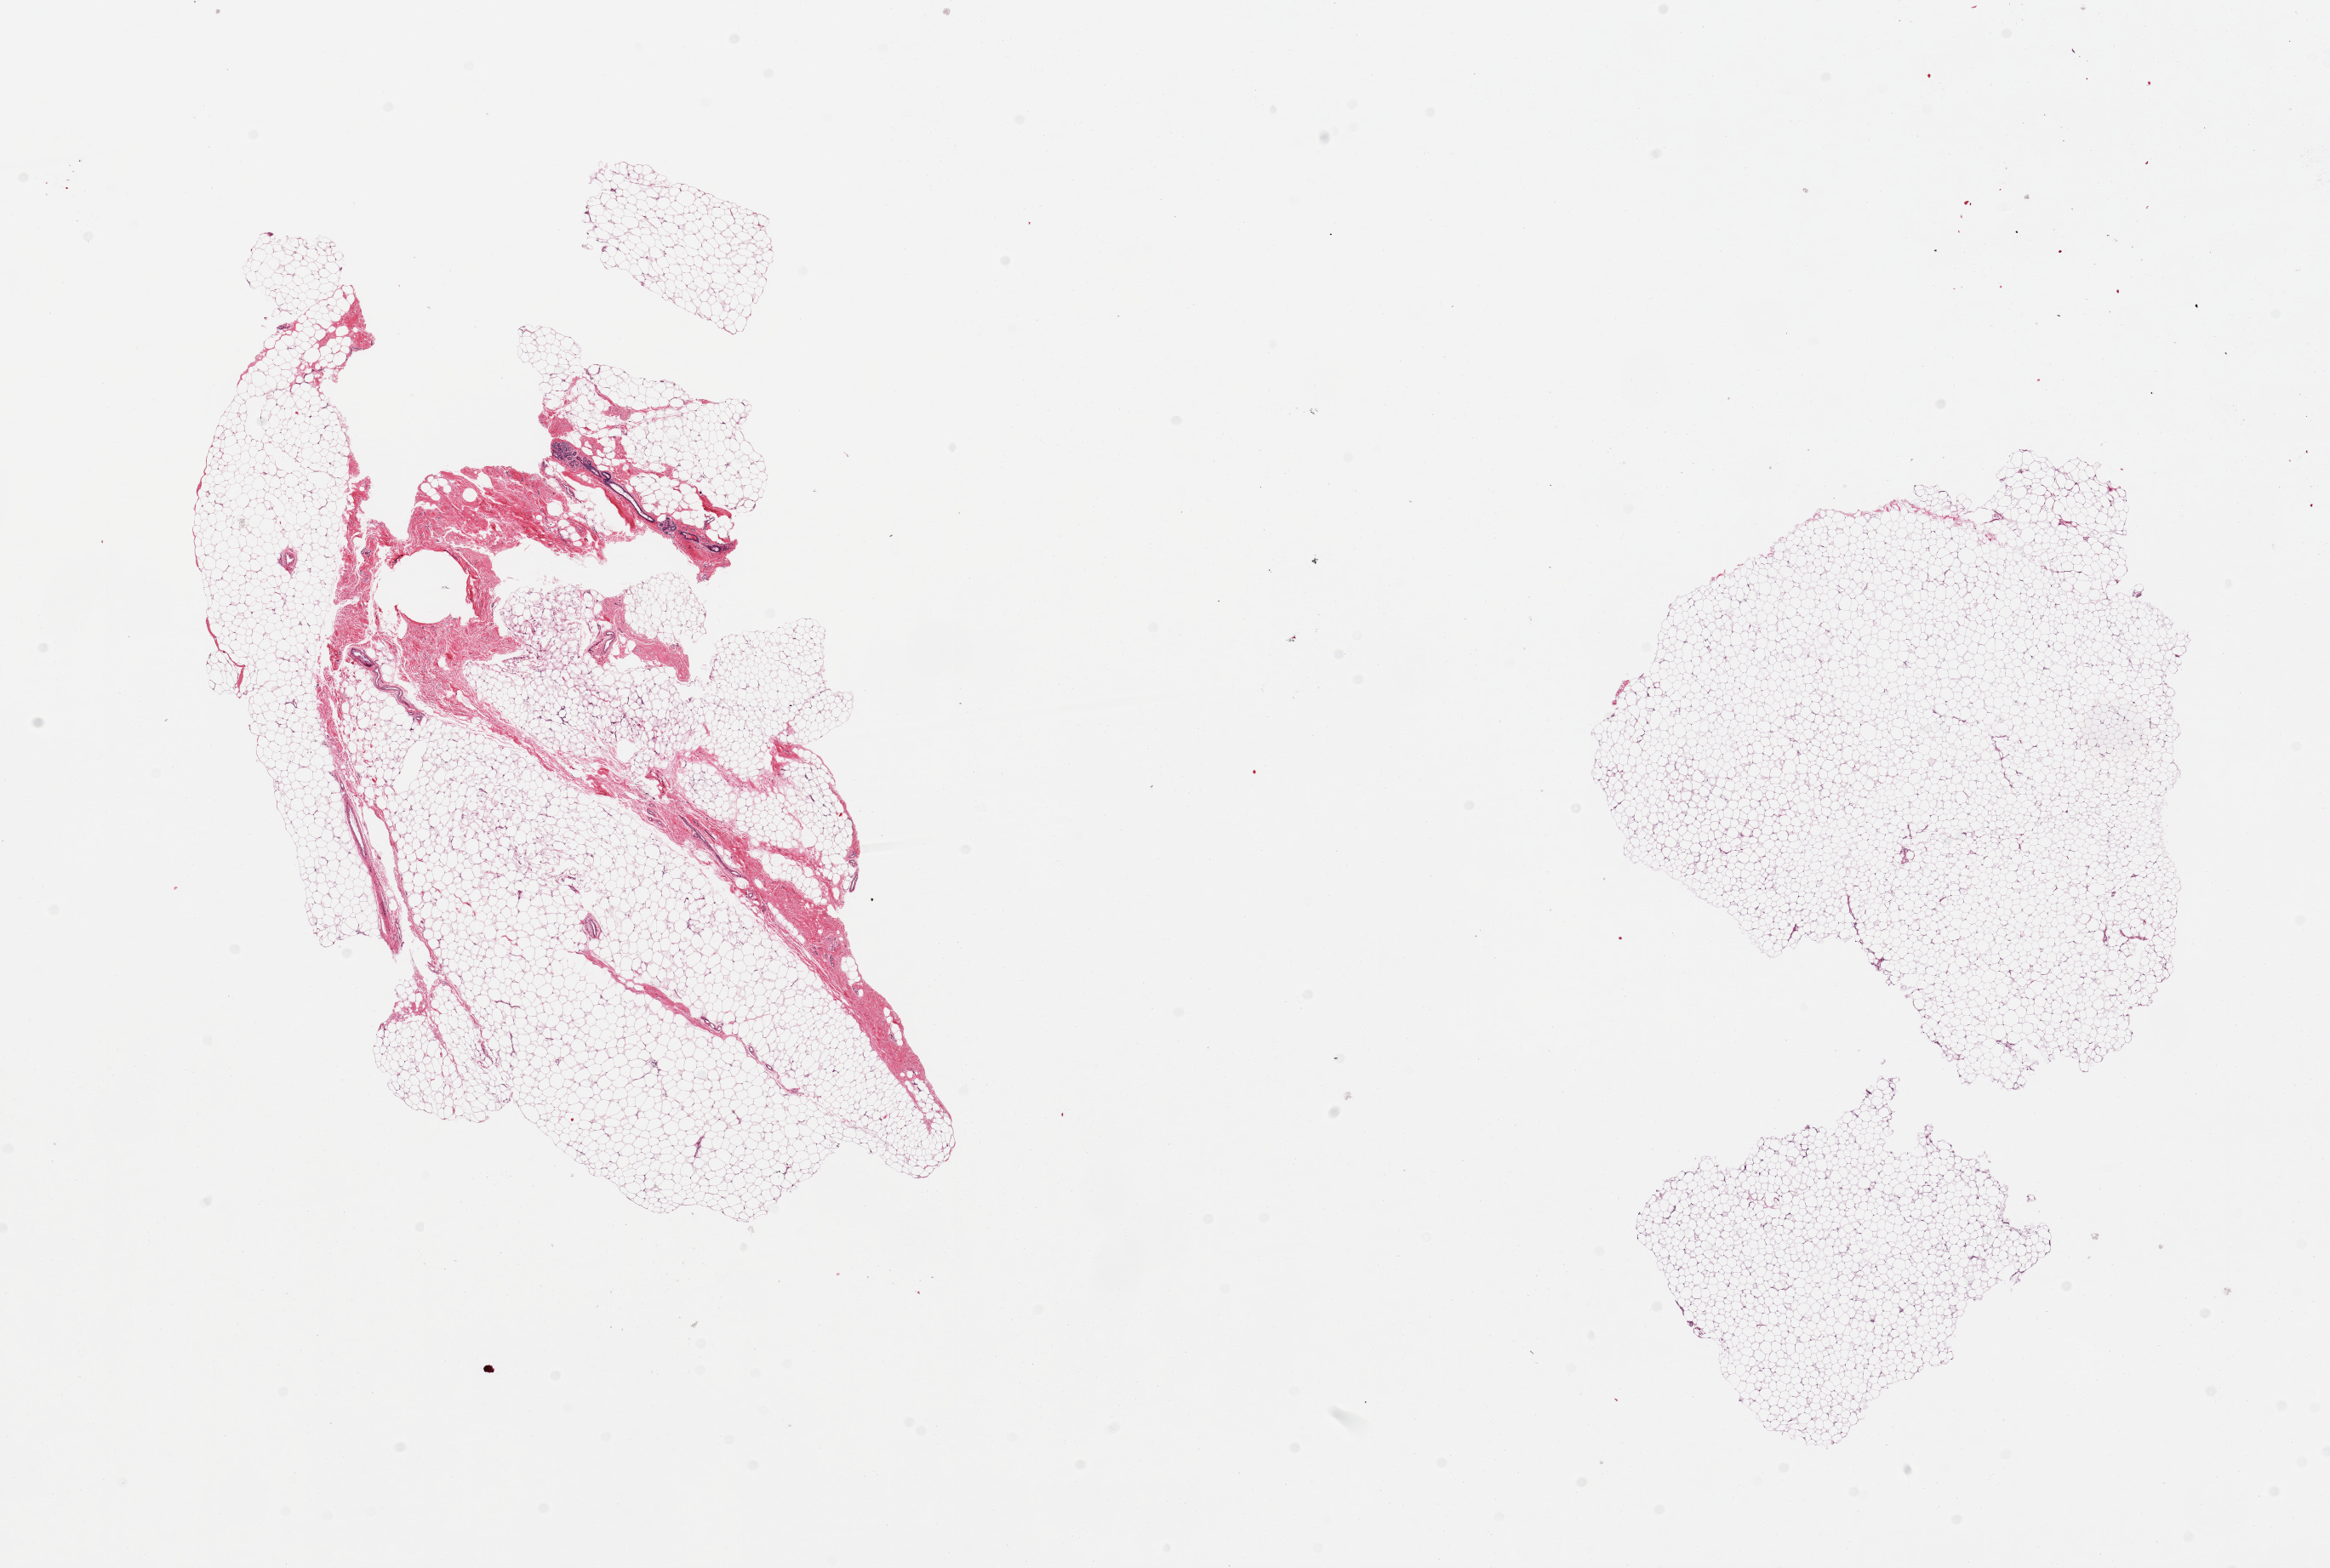
Whole-slide image, hematoxylin and eosin (H&E) stain, whole scanned area (about 21.7 x 14.6 mm, from a 20x scan) shown as a low-resolution overview, PAXgene-fixed, paraffin-embedded tissue, sampled site (target tissue): breast, tissue donor sample.
Reviewer comment on this tissue sample: 2 pieces; 90% fat with focal ductal-lobular focus on 1; all fat on other piece.